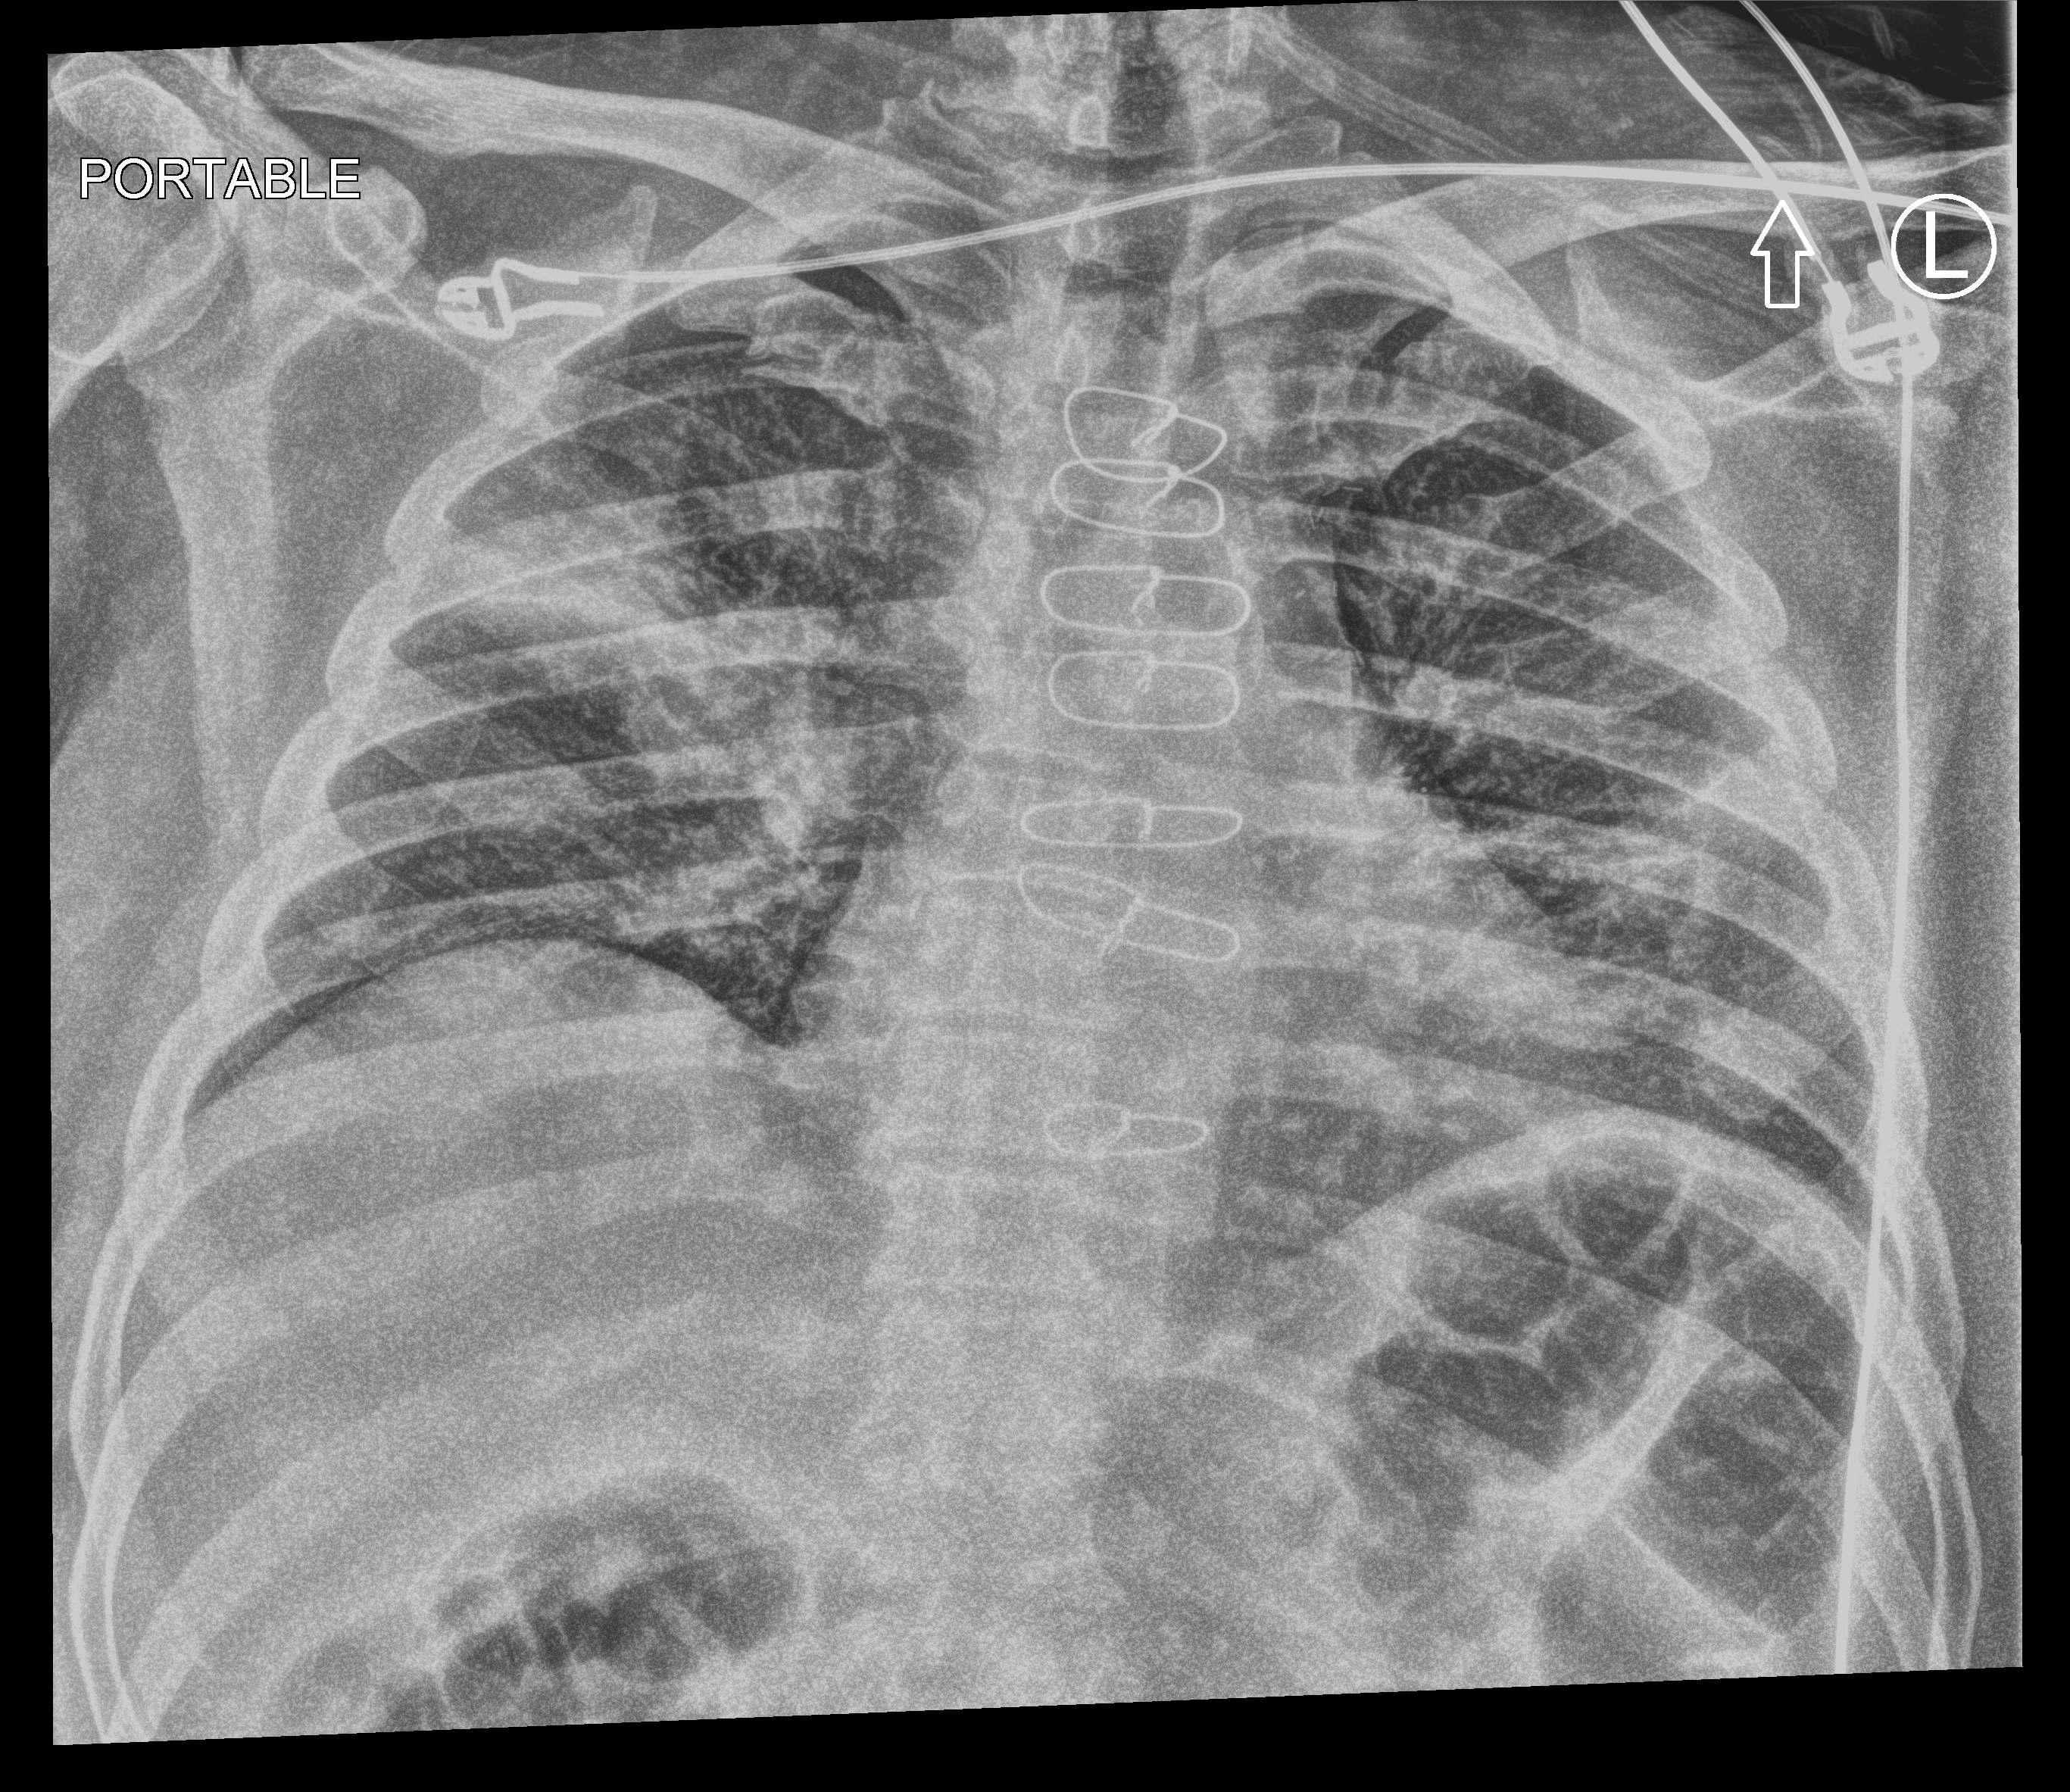
Bedside chest radiograph (computed radiography); anteroposterior (AP) projection. Patient hospitalised with COVID-19; male, aged 60–74 years.
Hospital-stay facts (about this admission, not read from this image; timing relative to this image not recorded):
- admitted to intensive care during this hospital stay: yes